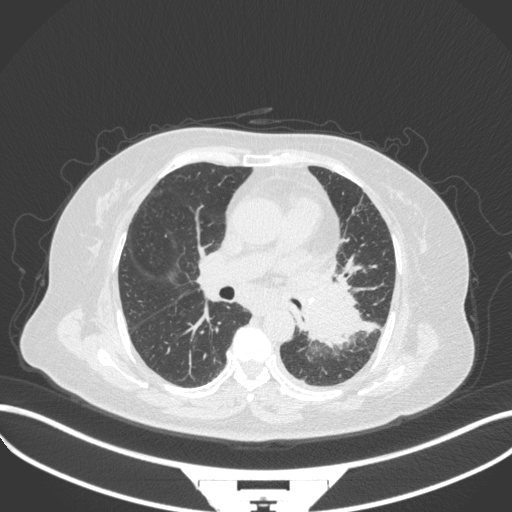
Chest CT, one axial slice. Slice 191 of 328 in the series (ordered by position). 120 kVp. Lung window (W 1500 / L -600 HU). 1 mm slice thickness. 512 × 512 image matrix, field of view 400 × 400 mm. Patient: female, 69 years. Case-level facts recorded for this patient, not image findings: clinical TNM (as recorded): T2b N3 M1.
Structures marked on this image (rectangle marked by the reading radiologist):
- lung tumour (recorded histology: adenocarcinoma): box from (x=294, y=278) to (x=364, y=350) px